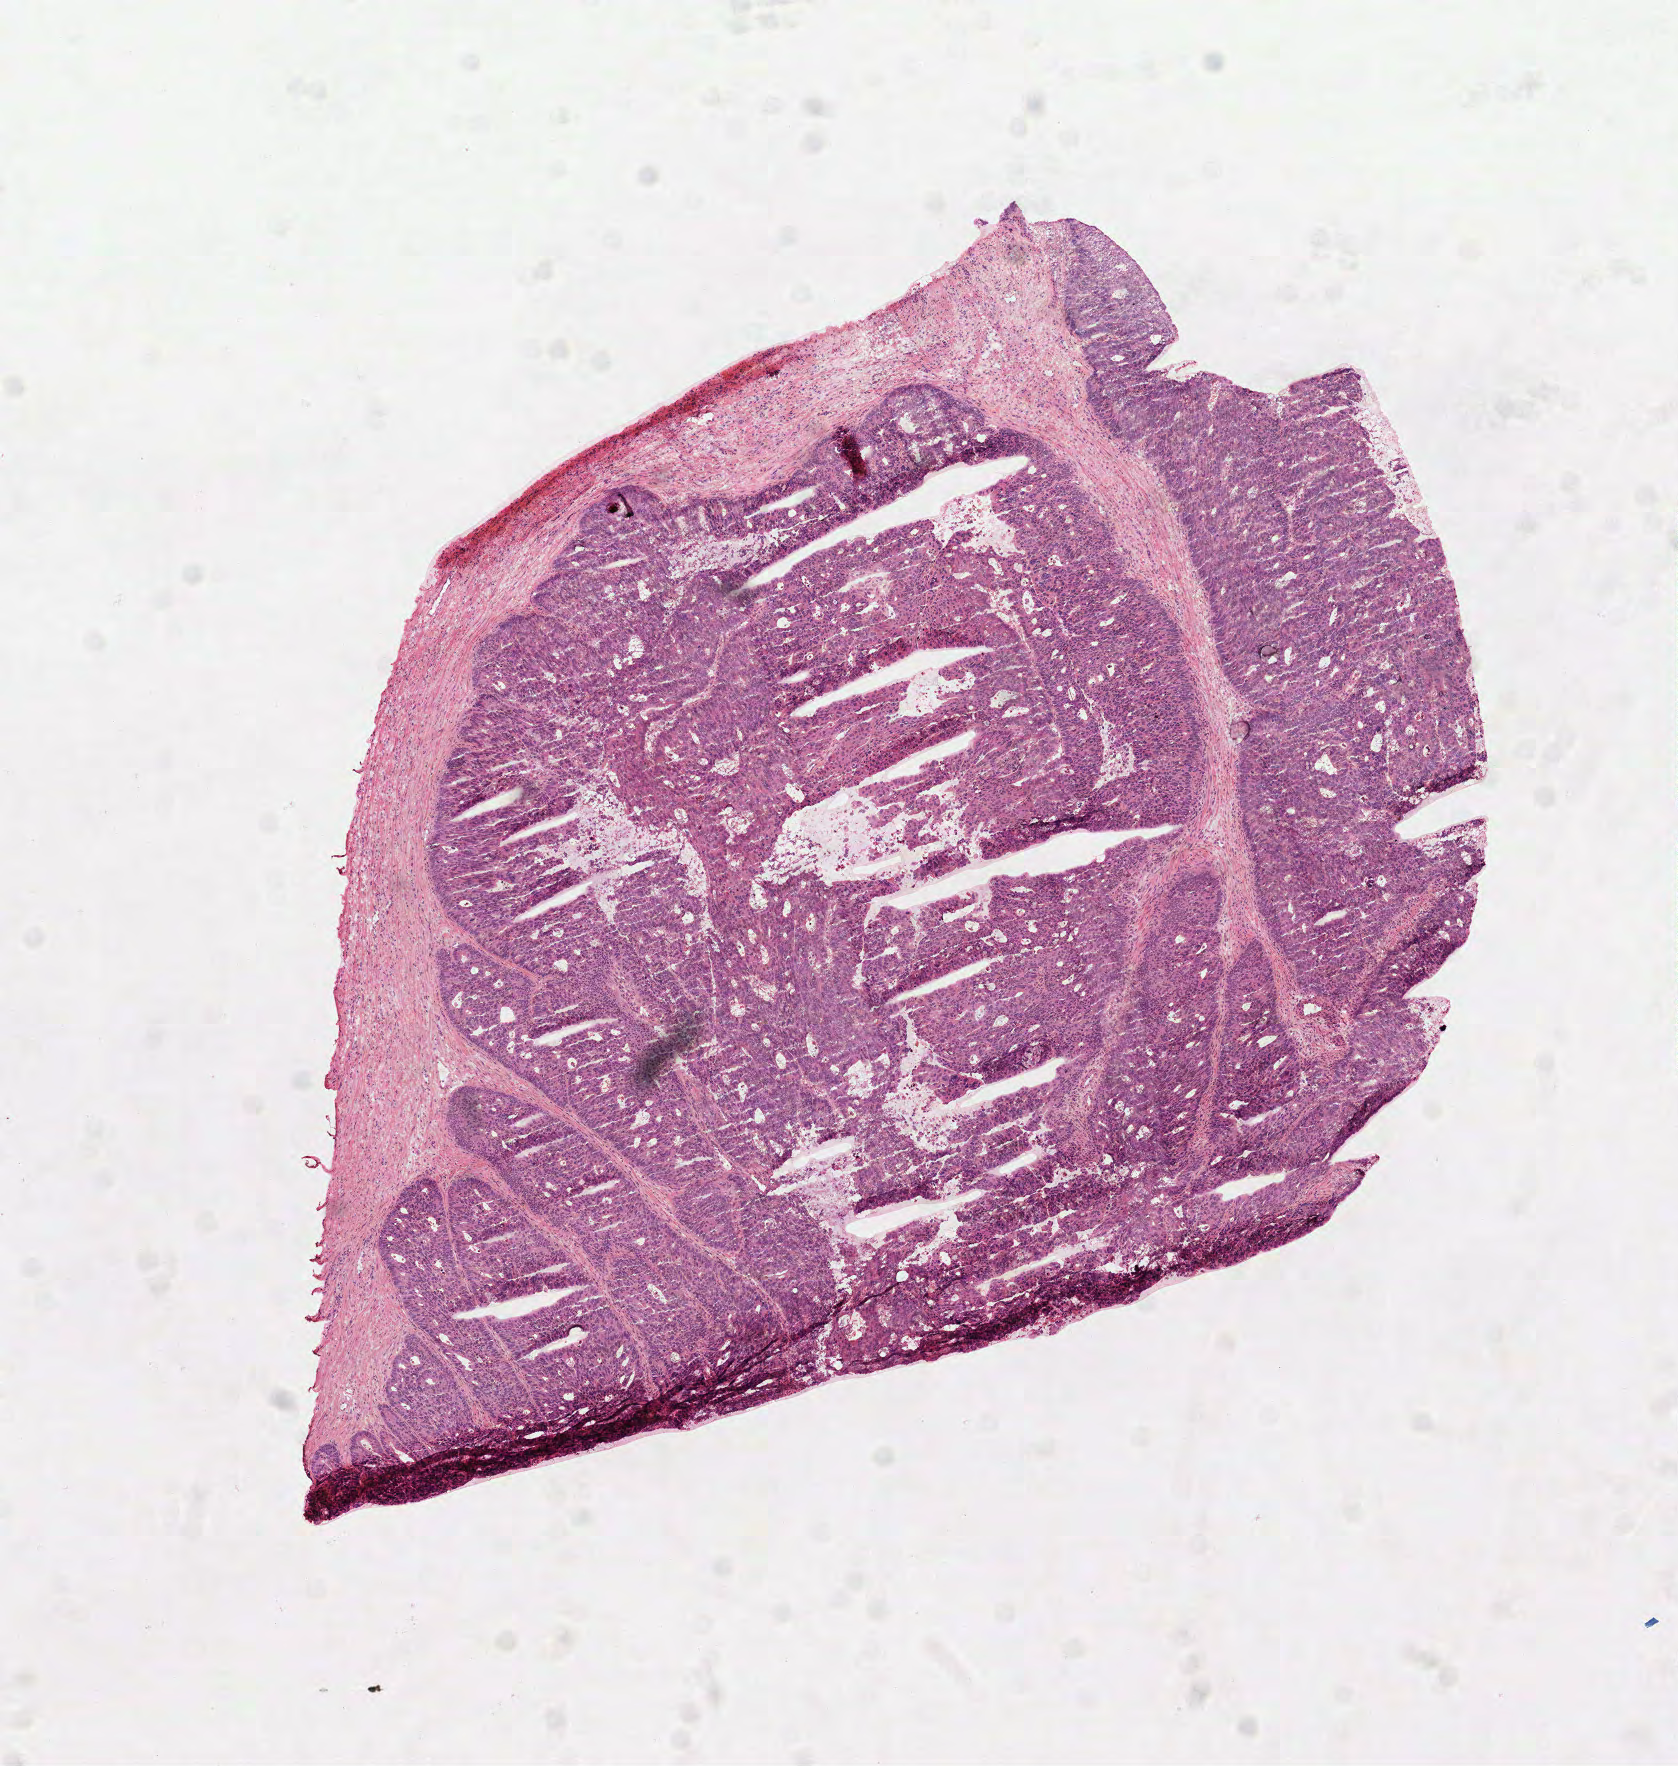
H&E whole-slide image — shown as a low-resolution overview of the whole scanned area (about 6.8 x 7.1 mm, from a 40x scan); frozen section from the top of the tissue portion; colon, primary tumour sample. Female, age 79 years at initial diagnosis. Pathologist review of this section (percent, as recorded): tumour cells 100%, tumour nuclei 85%, normal cells 0%, stromal cells 0%, necrosis 0%. Inflammatory infiltration, as recorded: lymphocyte infiltration 5%, monocyte infiltration 1%, neutrophil infiltration 2%.
* histologic diagnosis: Adenocarcinoma, NOS
* TNM: T3 N2 M0
* AJCC pathologic stage: IIIB
* lymph nodes positive (case pathology): 10 of 14 examined